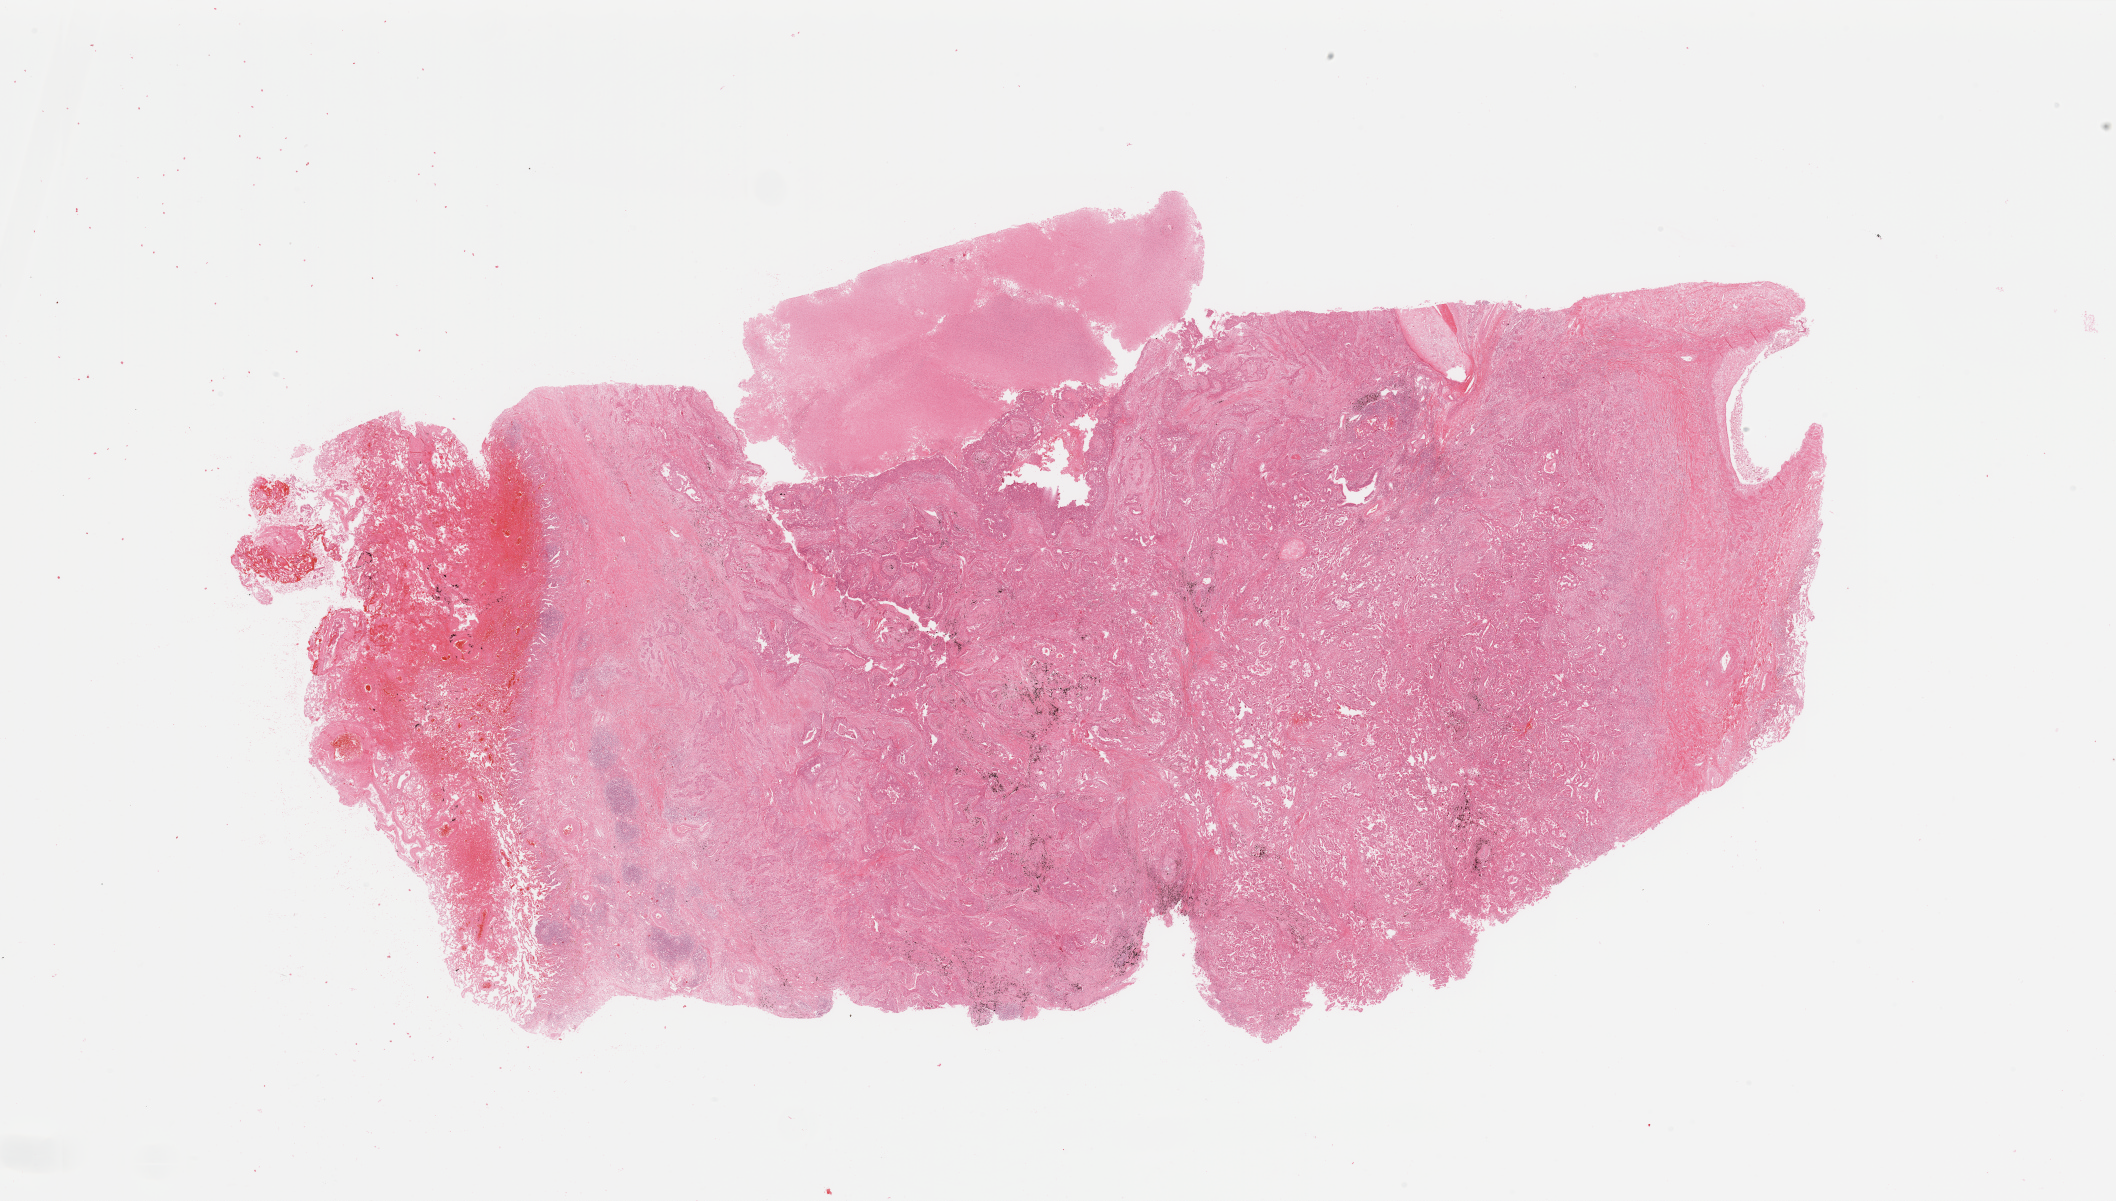
Whole-slide histology image, H&E-stained, low-resolution overview of the scanned area, about 33.5 x 19.0 mm. Tumour tissue sample, lung. 59-year-old male patient. Histologic grade: G3 (poorly differentiated).
- AJCC pathologic stage: IIA
- histologic diagnosis: Adenocarcinoma, NOS